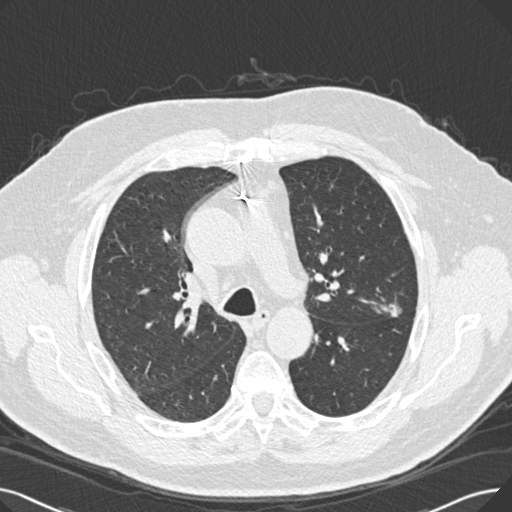
Low-dose screening chest CT, one axial slice; position 175 of 269 along the scan axis; reconstruction kernel B30f; lung window (W 1500 / L -600 HU); 512 × 512 image matrix, field of view 370 × 370 mm.
Structures marked on this image (expert manual segmentation):
- lesion 1 (tumor, upper lobe of left lung): bounding box <387,303,401,317> (left, top, right, bottom; pixels)